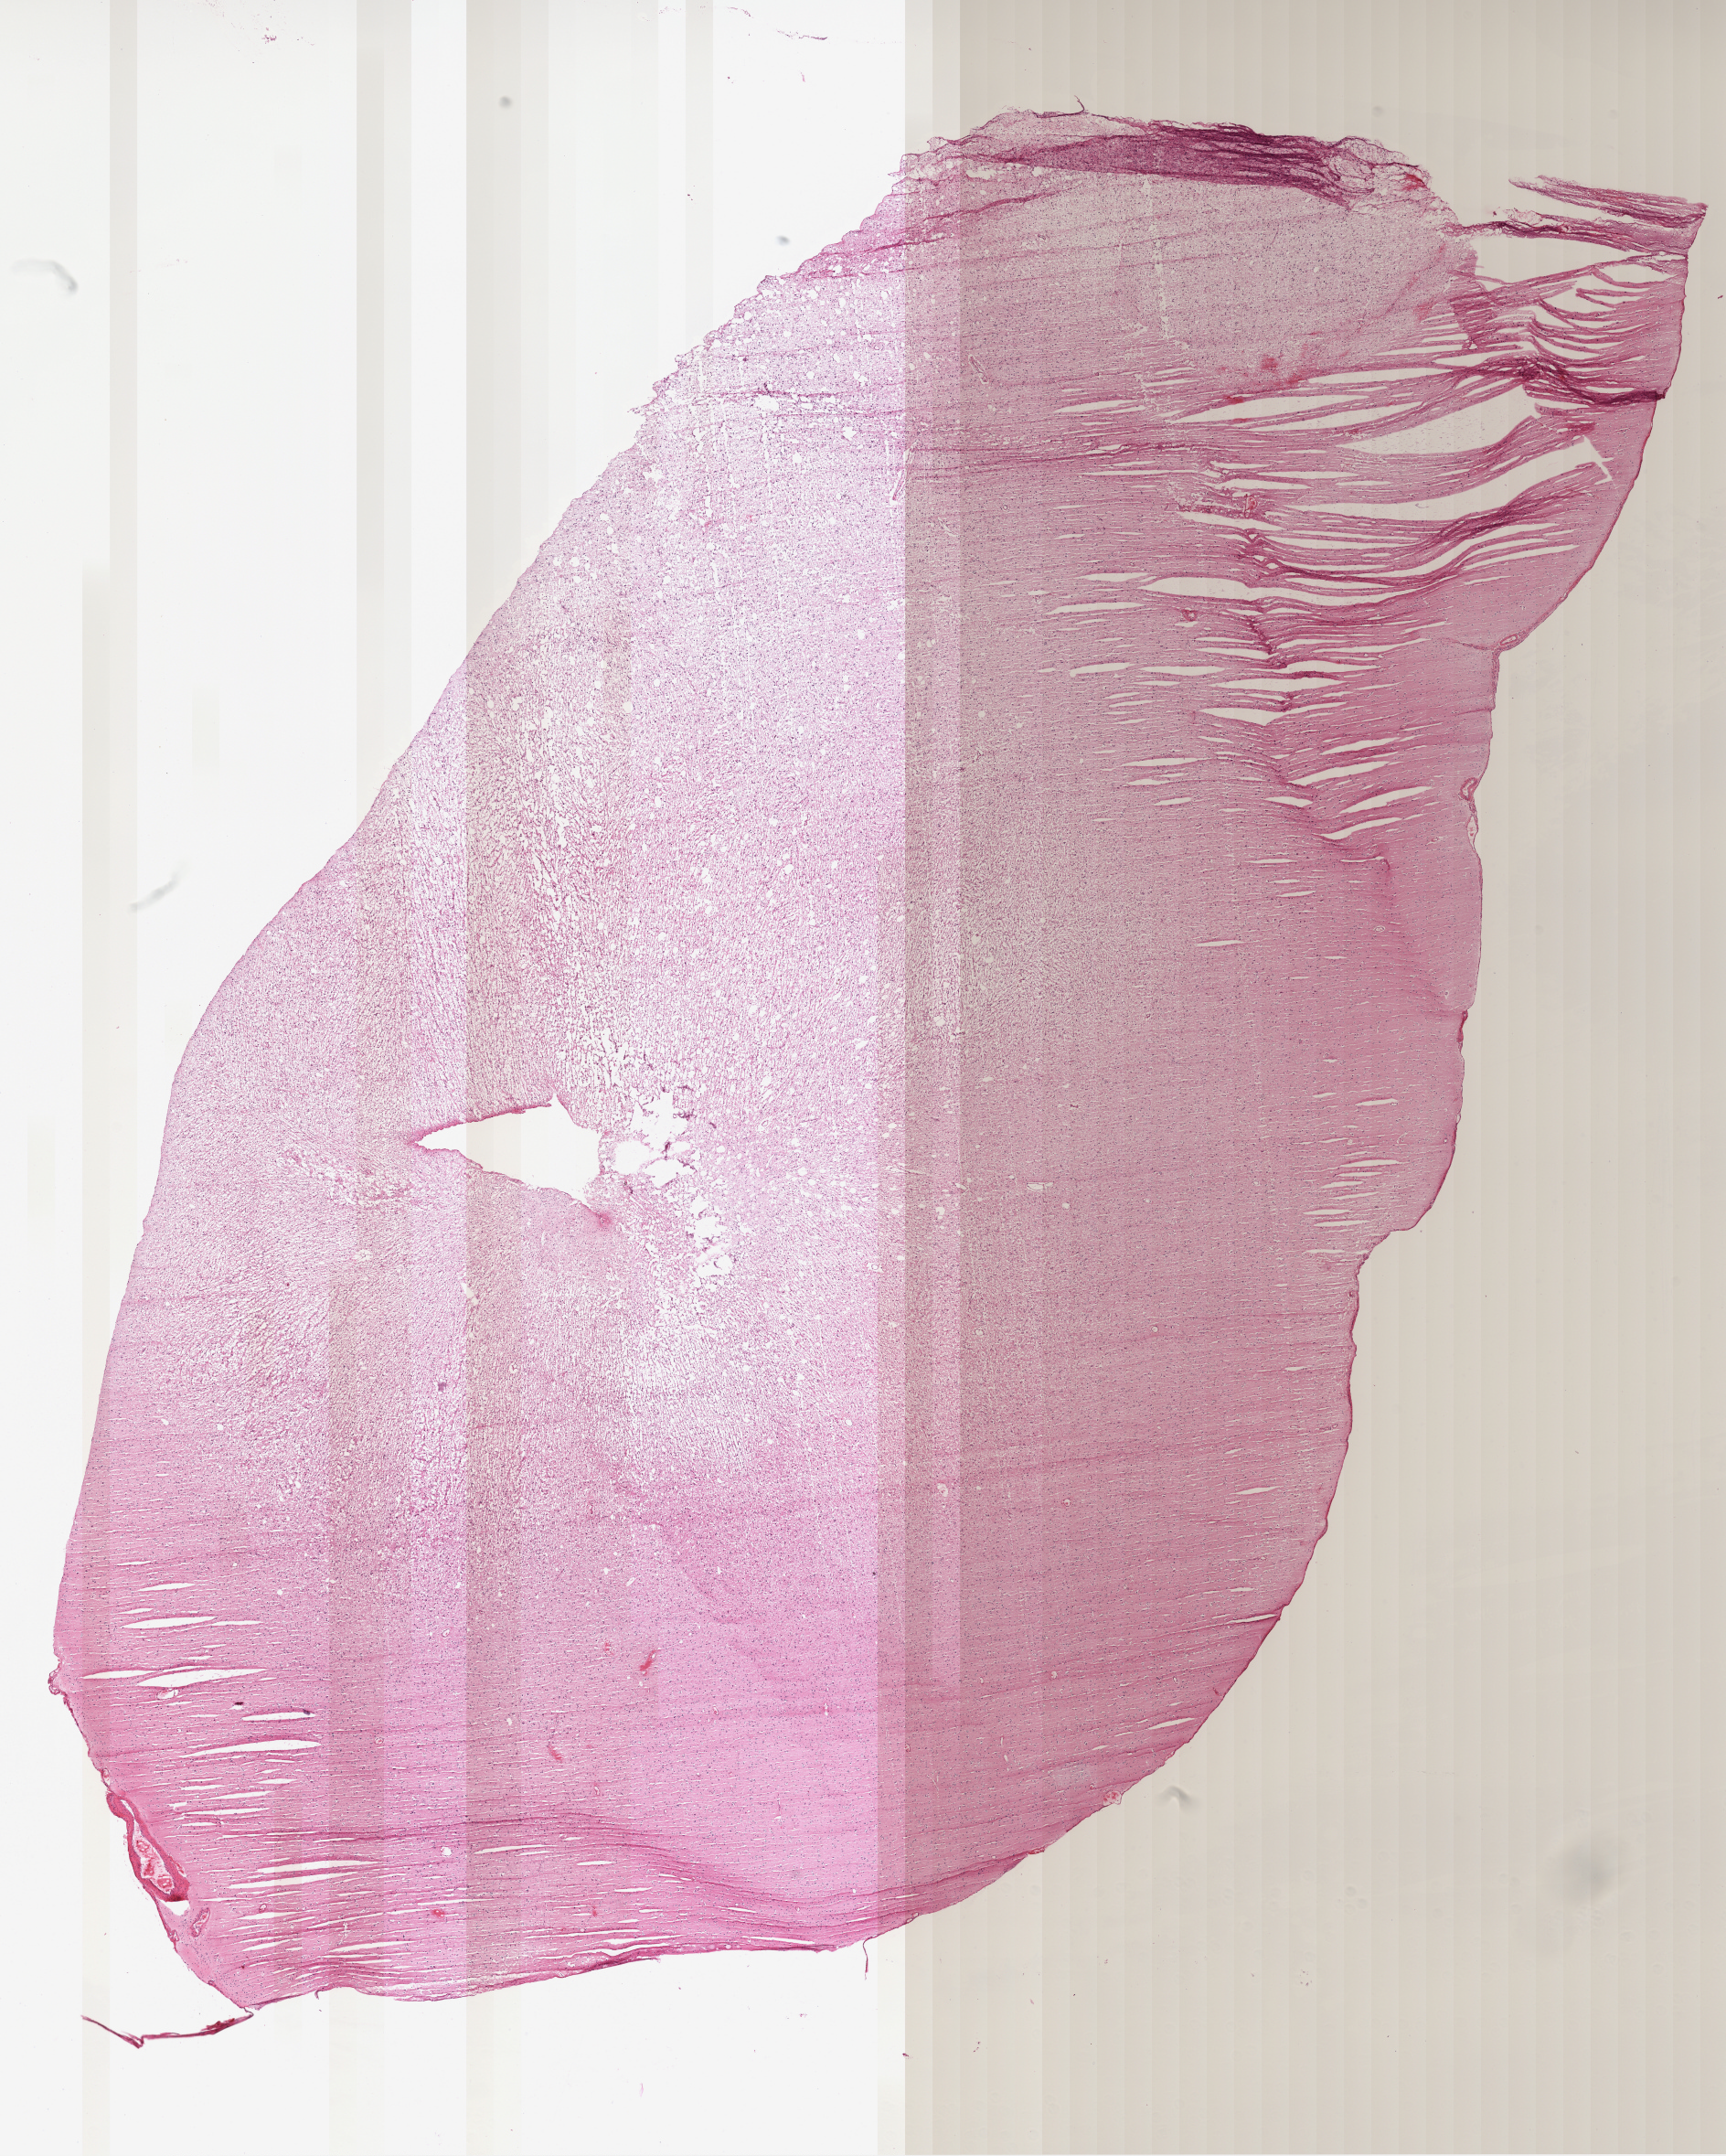
Whole-slide histology image, H&E, whole scanned area (about 15.2 x 19.0 mm, from a 40x scan) shown as a low-resolution overview; formalin-fixed paraffin-embedded (FFPE) diagnostic section; primary tumour sample from the brain. Patient: male, age at initial diagnosis 41 years. Histologic grade: G2 (moderately differentiated).
Histologic diagnosis: Mixed glioma (cerebrum).